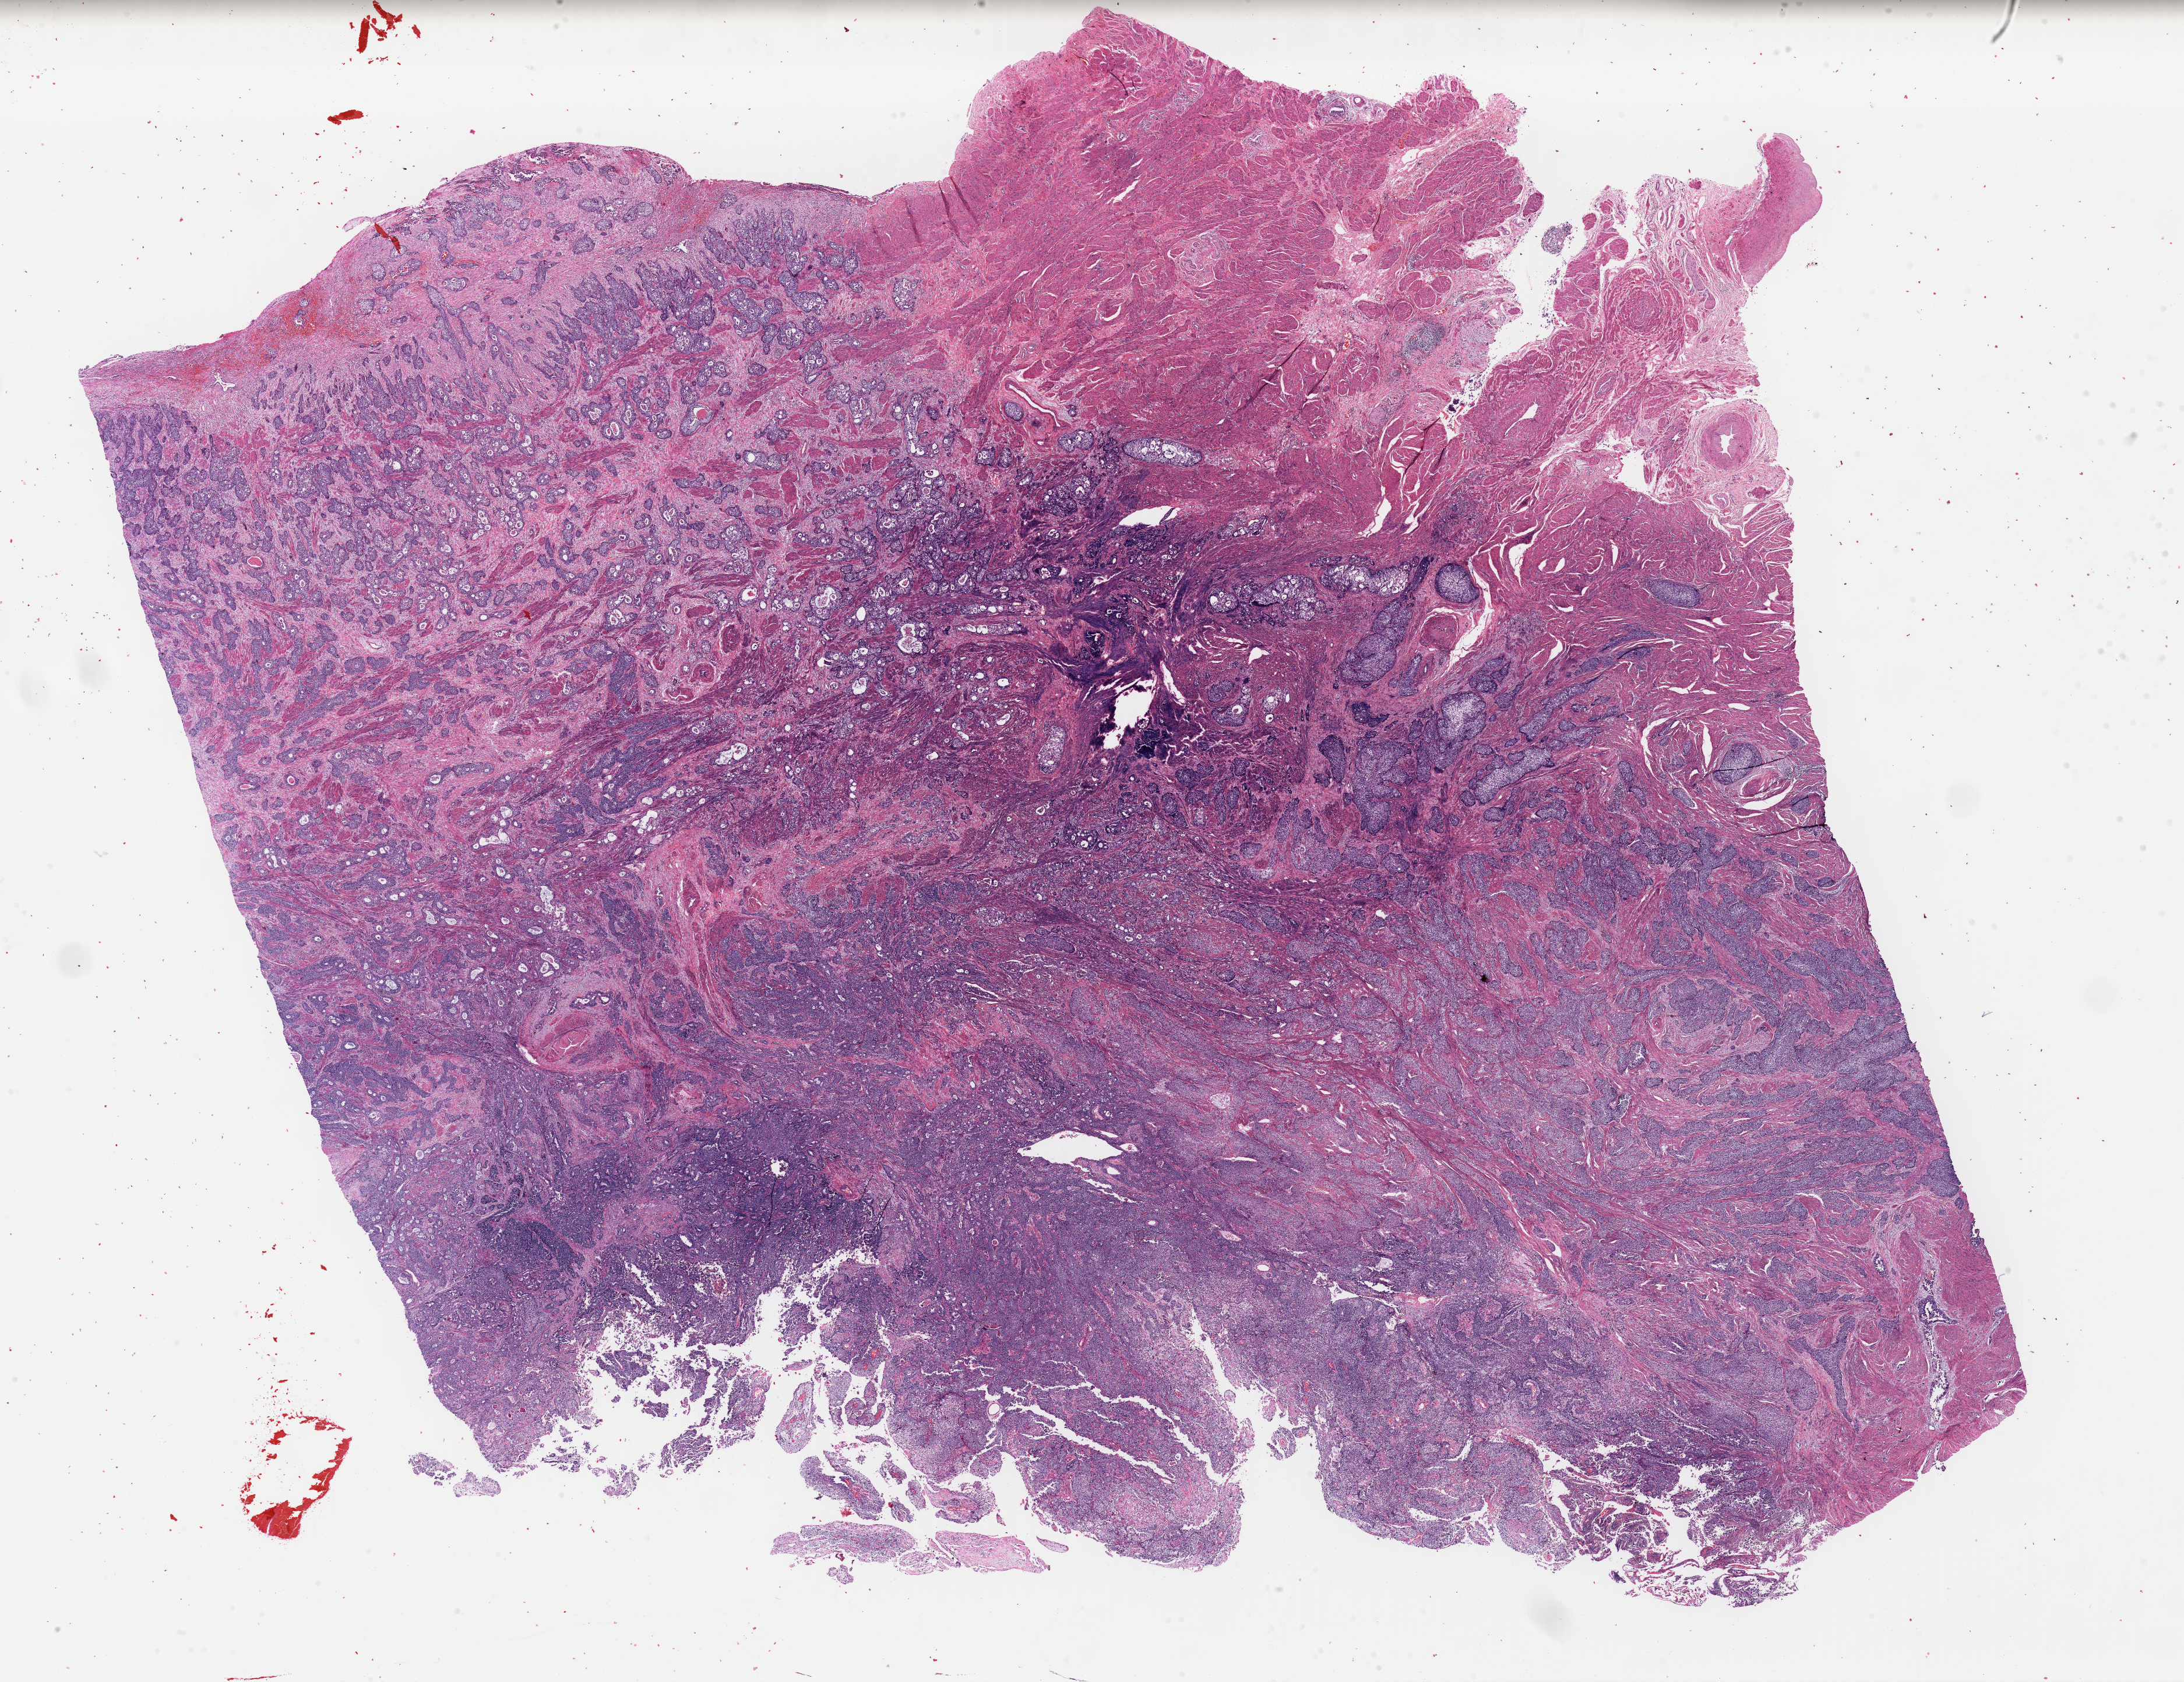
Hematoxylin and eosin (H&E) stained whole-slide image, a low-resolution overview of the entire scanned area, about 29.6 x 22.8 mm (from a 40x scan); formalin-fixed paraffin-embedded (FFPE) diagnostic section; sample: primary tumour, uterus. Female, age 75 years at initial diagnosis.
Histologic diagnosis: Carcinosarcoma, NOS. FIGO stage: IIIC1.